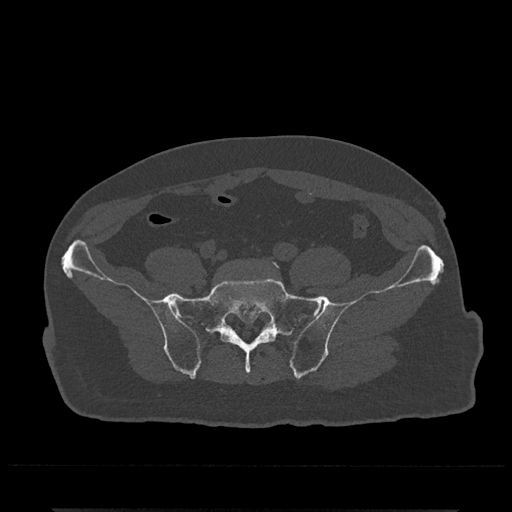
CT including the spine, one axial slice. Position 28 of 797 along the scan axis. Reconstruction kernel Br40s/3. 120 kVp. Bone window (W 1800 / L 400 HU). 0.5 mm slice thickness. 512 × 512 image matrix, field of view 393 × 393 mm. Patient: male, 67 years. Case-level facts recorded for this patient, not image findings: primary cancer: prostate.
Annotated regions visible in this slice (semi-automatic segmentation, software-assisted and operator-edited):
- L5 vertebra: bounding box (x1, y1, x2, y2) in pixels: (272, 260, 280, 268)